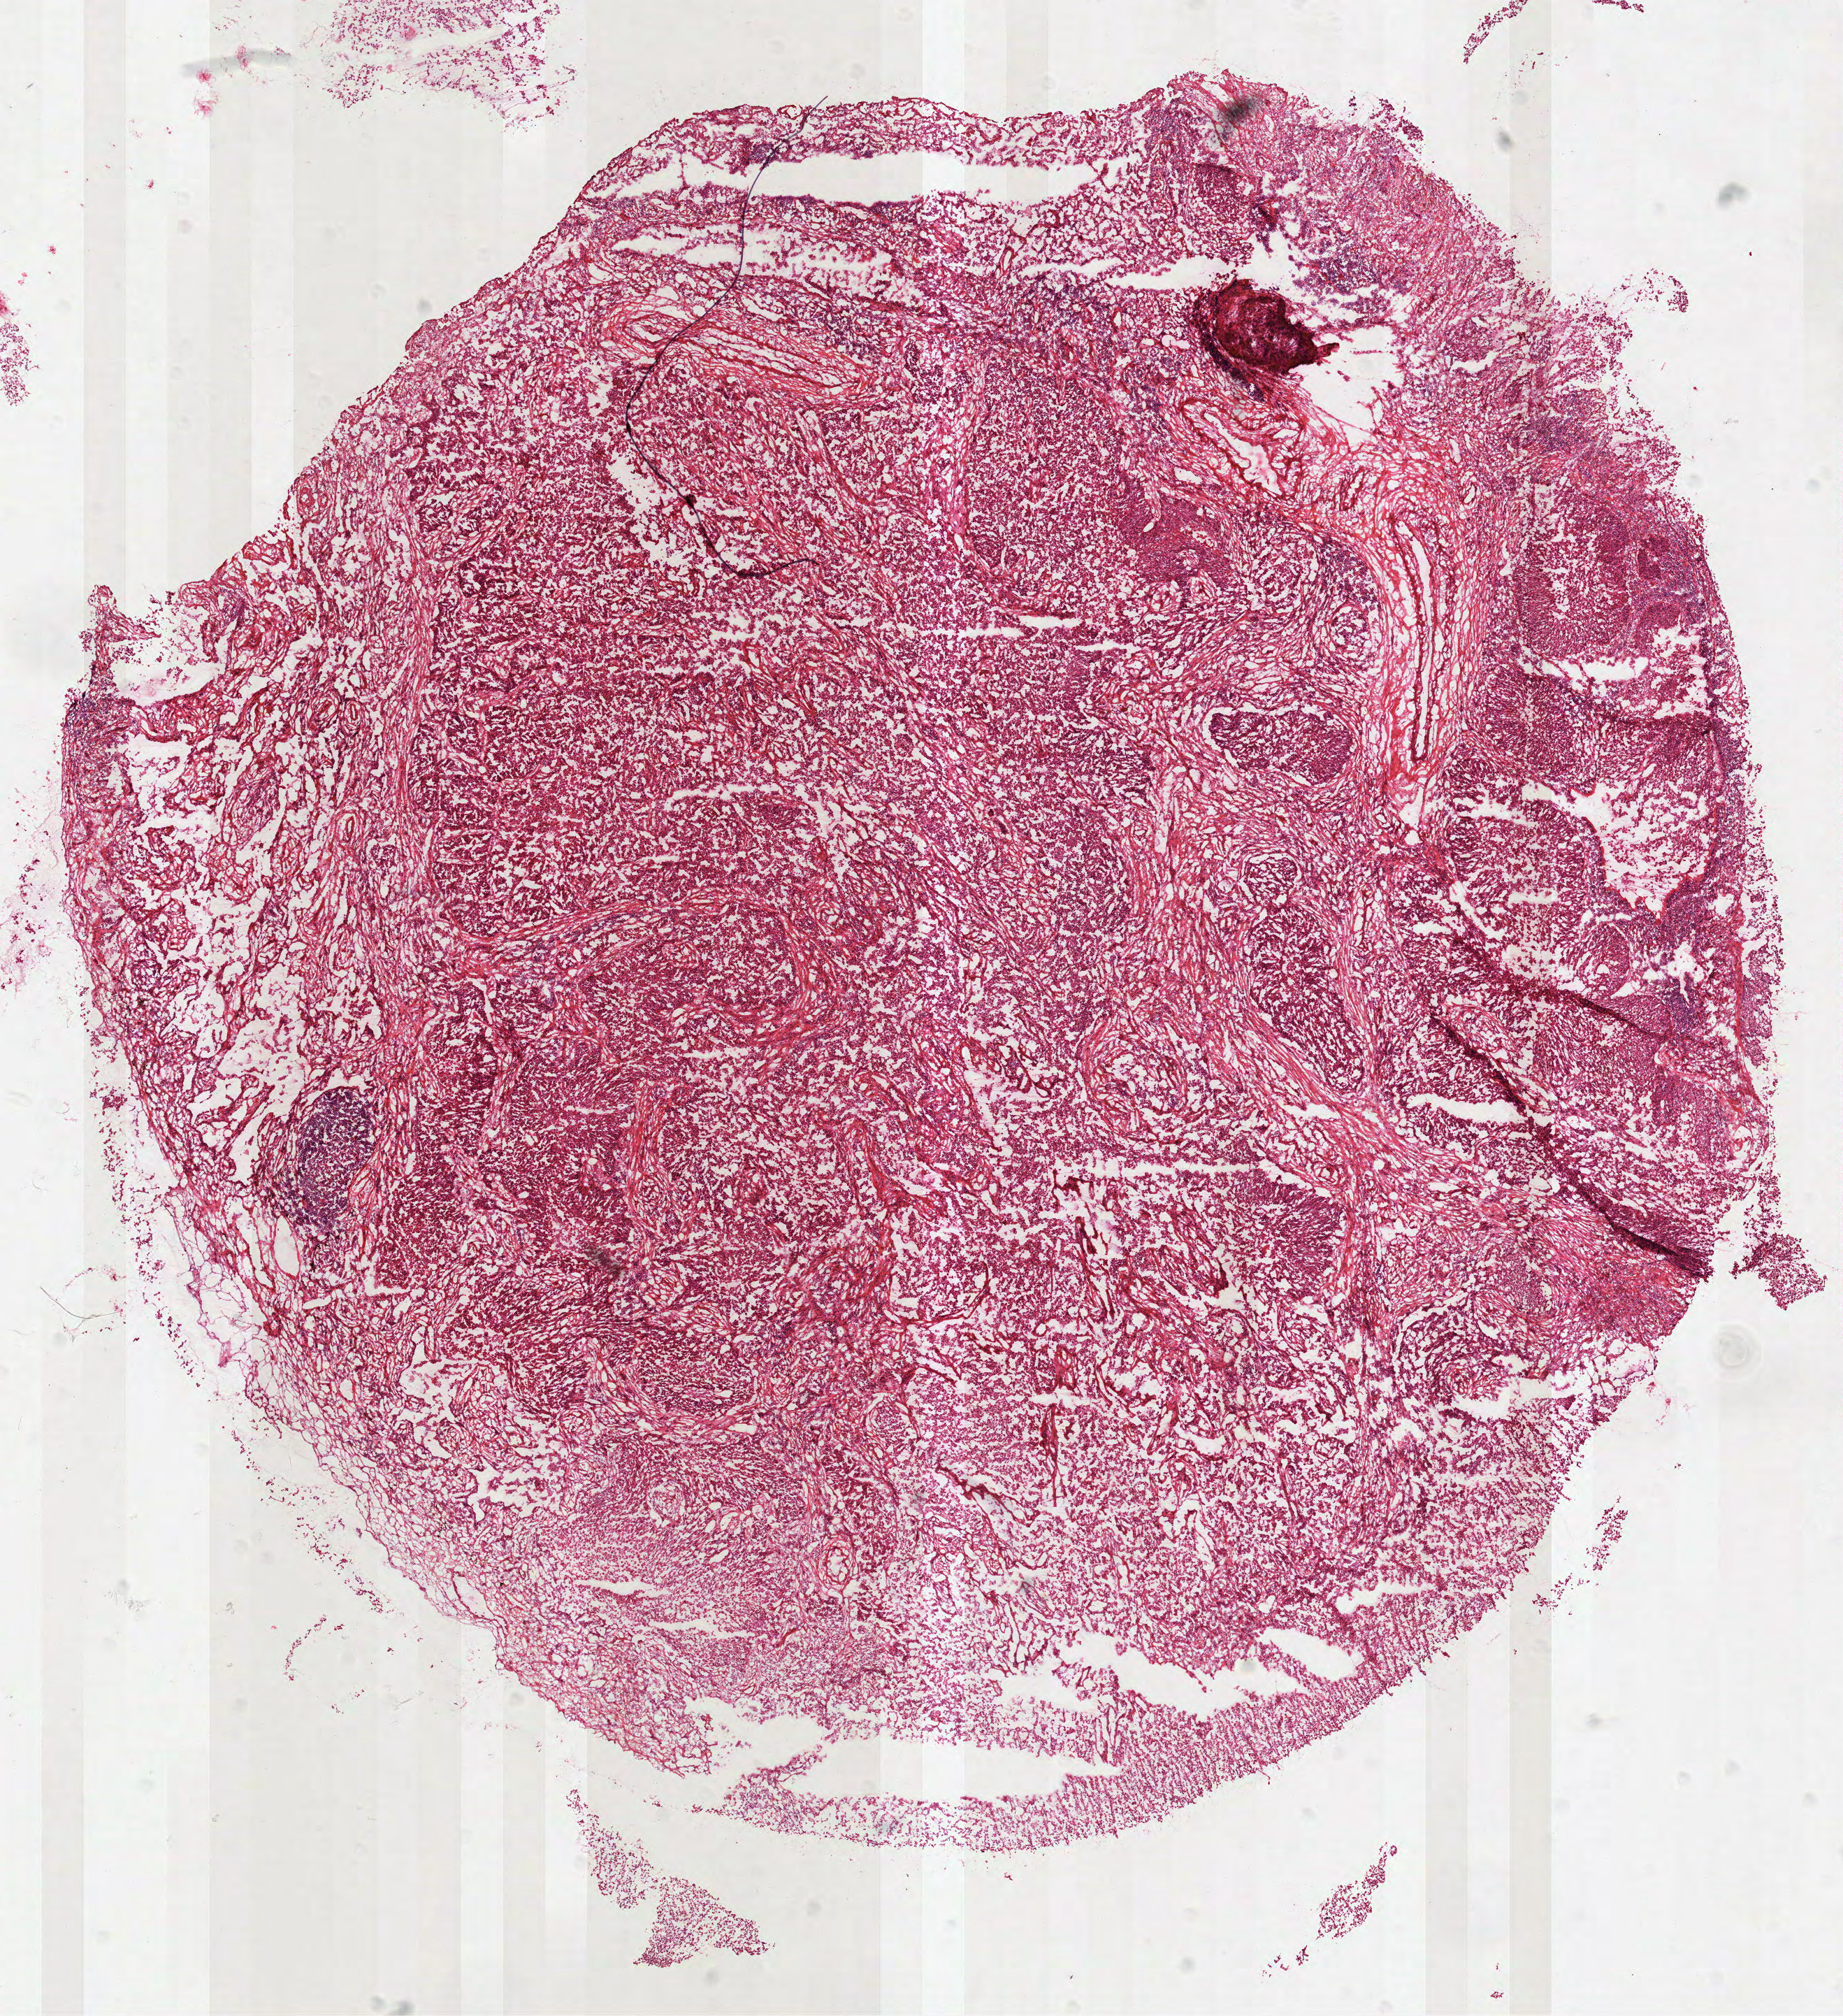
H&E-stained whole-slide image — a low-resolution overview of the entire scanned area, about 10.6 x 11.6 mm (acquisition: 40x scan), frozen section from the top of the tissue portion, lung, primary tumour sample. Patient: female, age at initial diagnosis 62 years. Slide review estimates, as recorded: tumour cells 85%, tumour nuclei 70%, normal cells 0%, stromal cells 10%, necrosis 5%.
• AJCC pathologic stage: IIIA (7th edition)
• laterality: right
• diagnosis: Squamous cell carcinoma, NOS (lower lobe, lung)